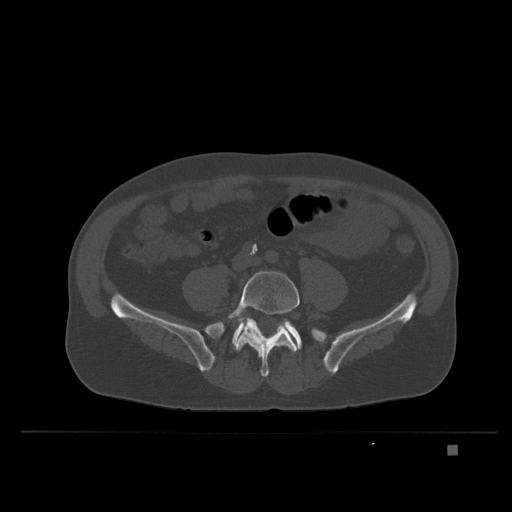
CT including the spine, one axial slice. Slice 55 of 435 in the series (ordered by position). Bone window (W 1800 / L 400 HU). 512 × 512 image matrix, field of view 434 × 434 mm. Male patient, age 73 years. From the clinical record (not read from this slice): primary cancer: skin.
Outlined on this slice (semi-automatically segmented with operator editing):
- L5 vertebra: bounding box [x1, y1, x2, y2] px = [228, 270, 300, 377]